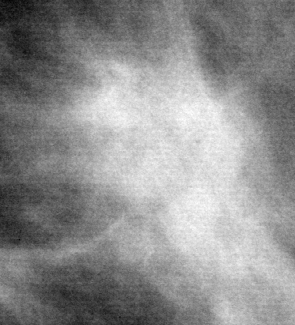
Cropped region of a digitized screen-film mammogram centred on a radiologist-marked abnormality; left breast; MLO view; BI-RADS breast density category 2 (scale 1–4).
Finding: mass, shape oval, margins spiculated; BI-RADS assessment category 5; subtlety rating 4 on a 1 (subtle) to 5 (obvious) scale; pathology result (as recorded, not read from the image): malignant.